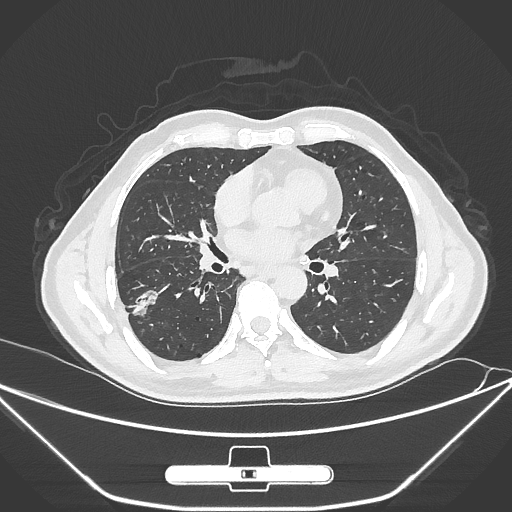
Chest CT, one axial slice. Slice 144 of 310 in the series (ordered by position). 120 kVp. Lung window (W 1500 / L -600 HU). 512 × 512 image matrix, field of view 398 × 398 mm. Patient: male, 71 years. Case-level facts recorded for this patient, not image findings: clinical TNM (as recorded): T1c N0 M0; histopathological grade: G2.
Annotated regions visible in this slice (bounding box drawn by a radiologist):
- lung tumour (recorded histology: adenocarcinoma): bounding box [x1, y1, x2, y2] px = [125, 279, 157, 326]